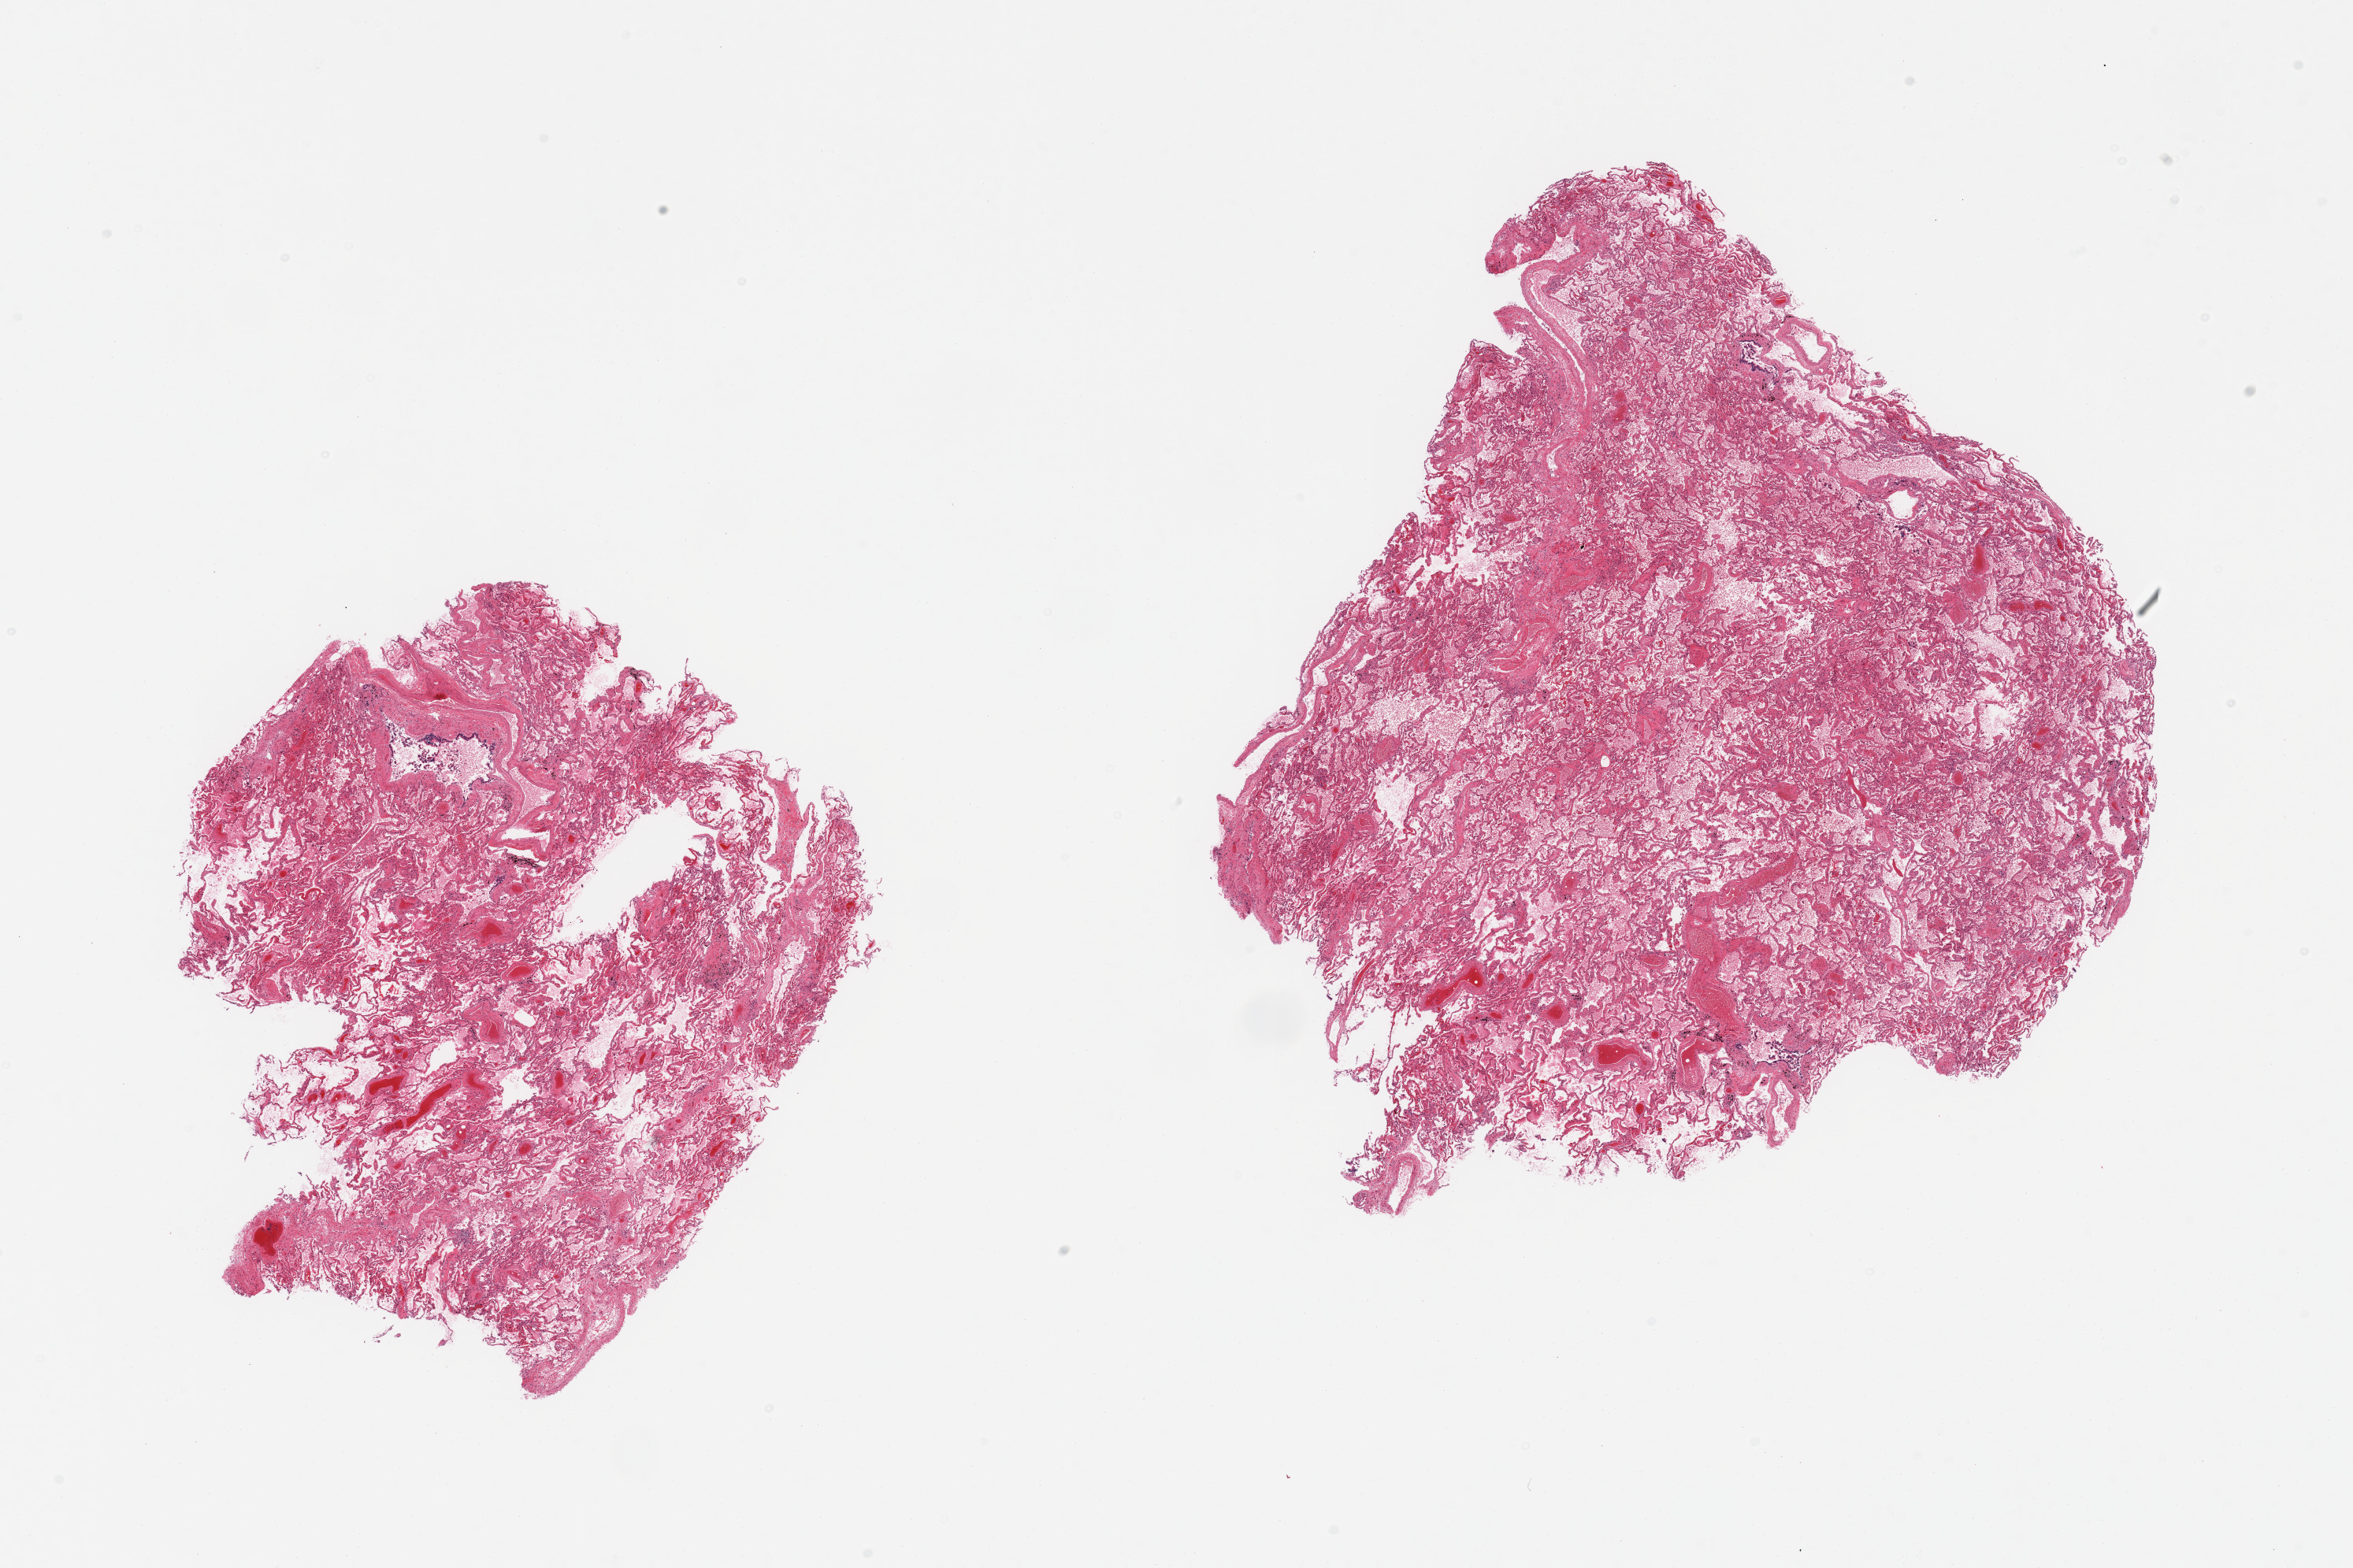
H&E whole-slide image, brightfield — whole scanned area (about 23.6 x 15.7 mm, from a 20x scan) shown as a low-resolution overview. PAXgene-fixed, paraffin-embedded tissue. Section of lung (target tissue). Donor tissue sample.
Reviewer comment on this tissue sample: 2 pieces; severe alveolar edema; focal interstitial fibrosis.